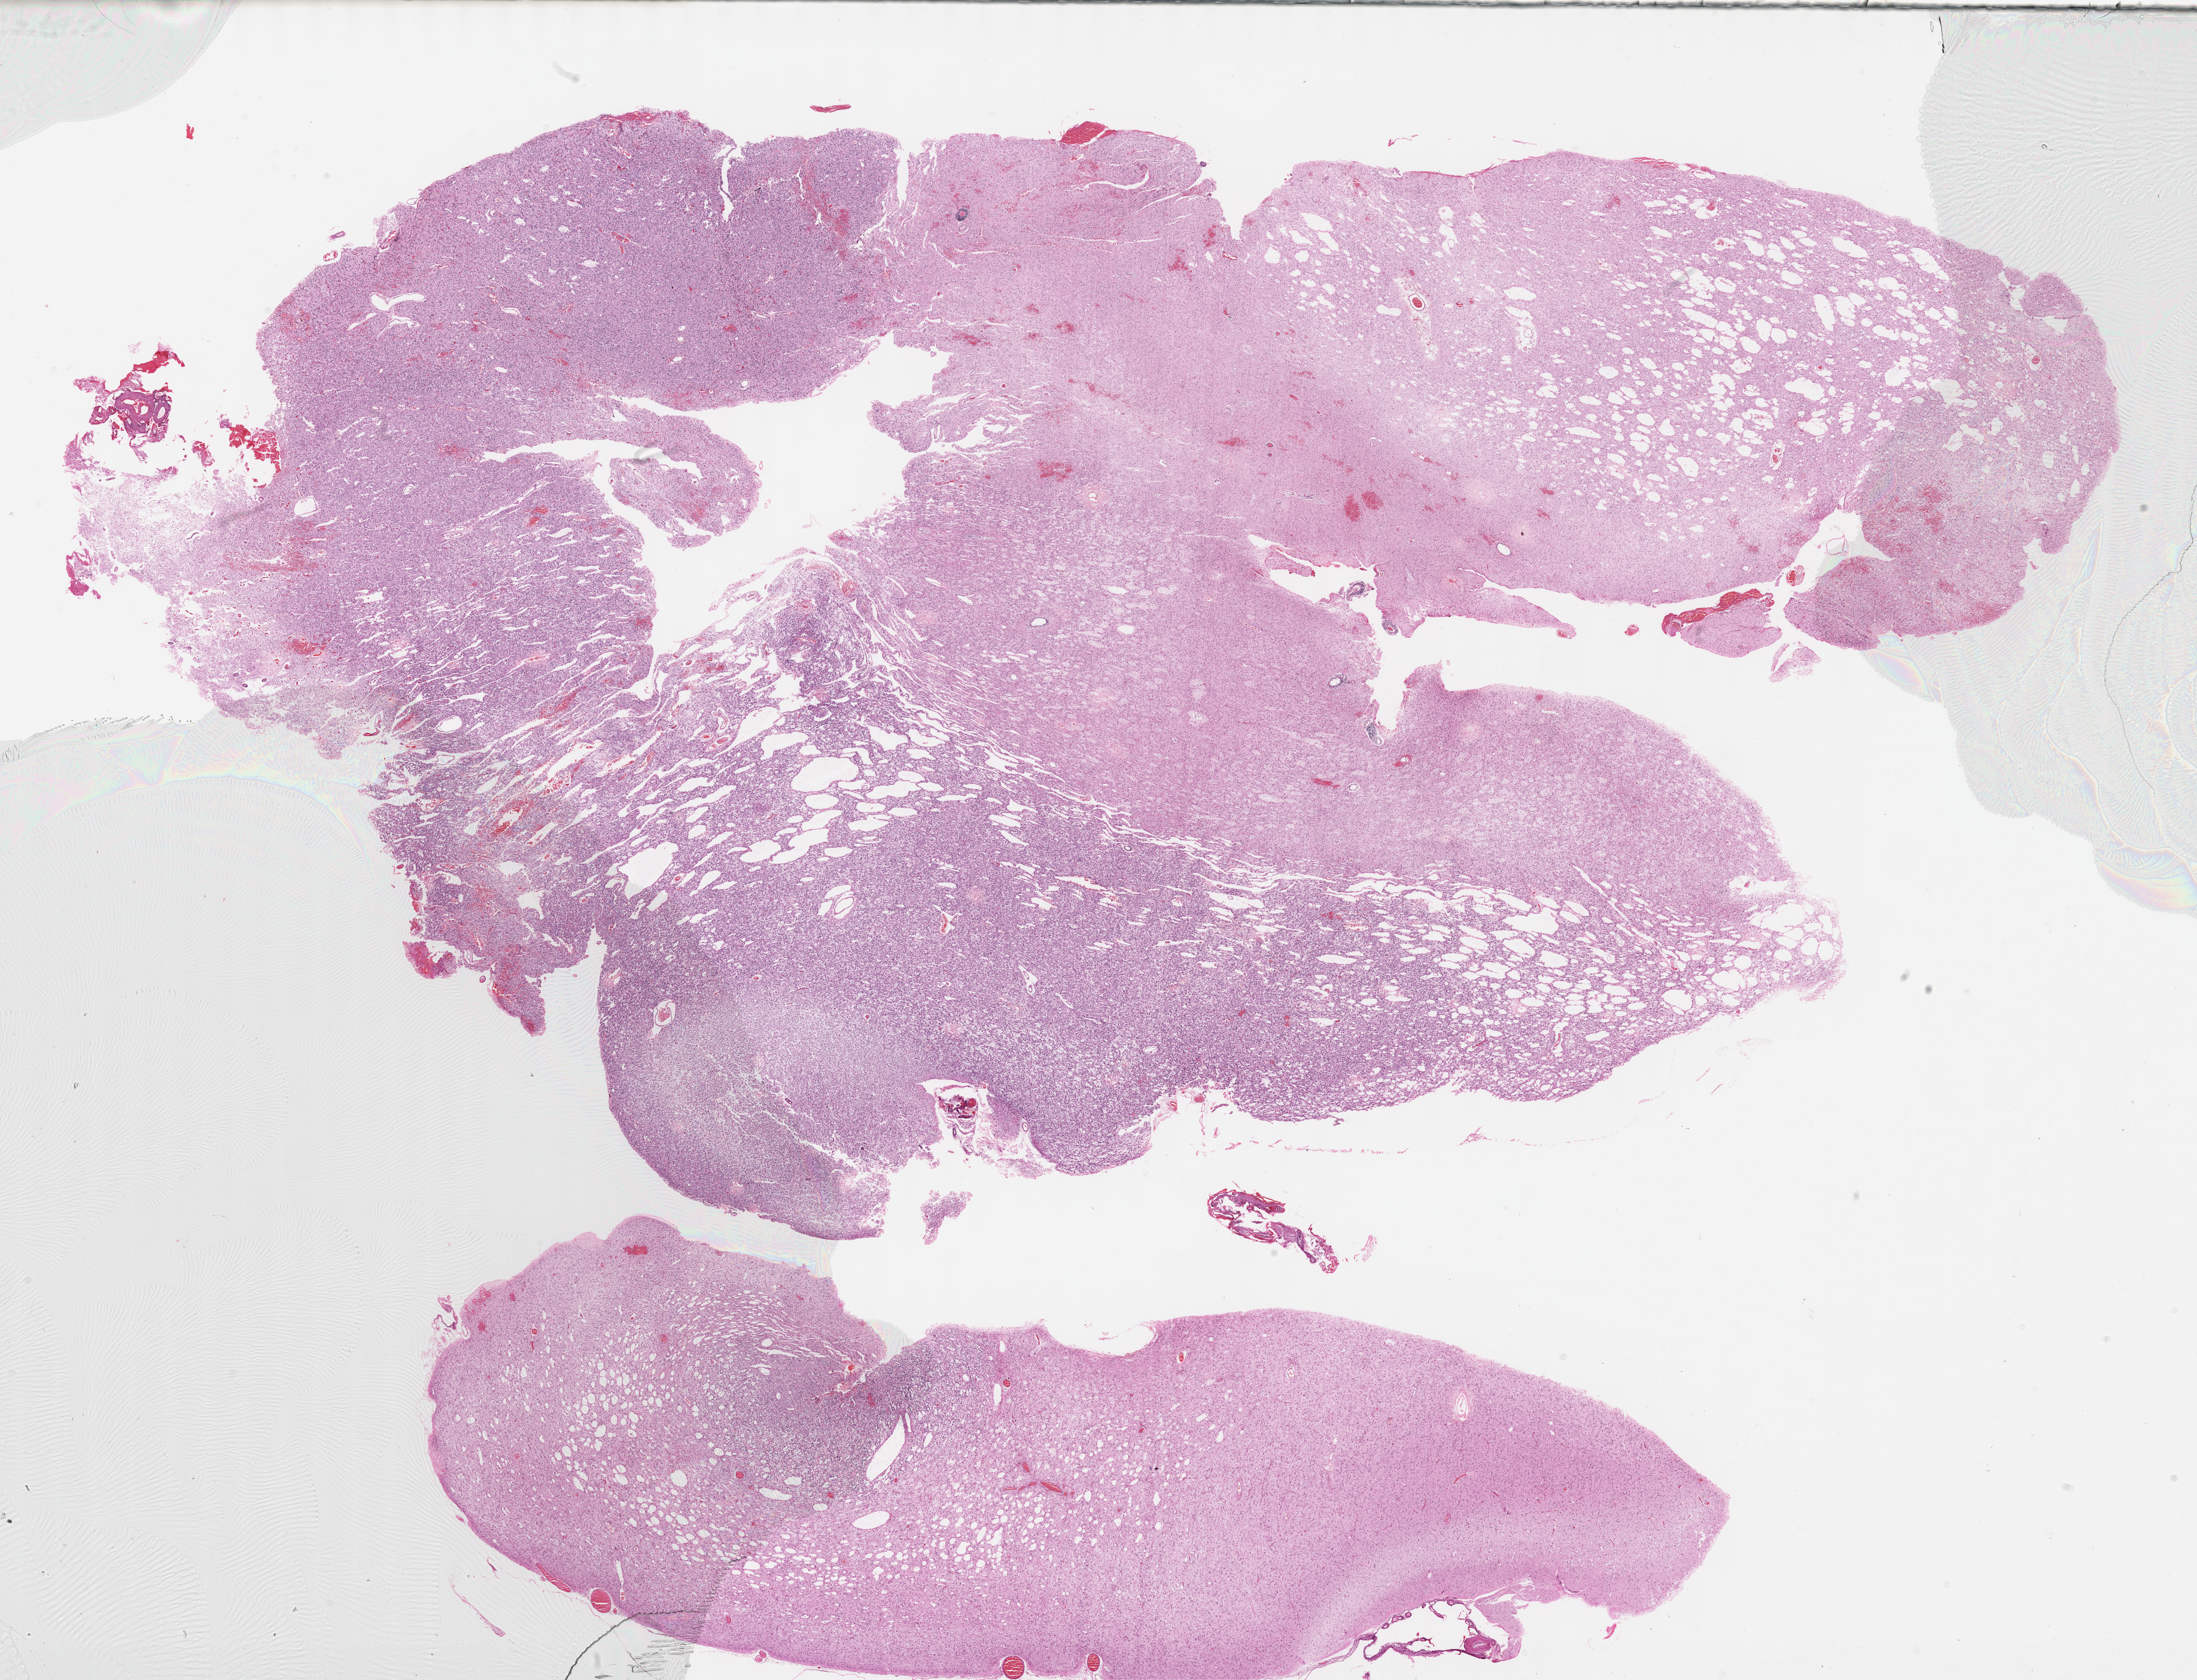
Whole-slide histology image, H&E-stained — a low-resolution overview of the entire scanned area, about 29.7 x 22.7 mm (from a 40x scan). Formalin-fixed paraffin-embedded (FFPE) diagnostic section. Primary tumour sample from the brain. Patient: female, age at initial diagnosis 25 years. Histologic grade: G2 (moderately differentiated).
• histologic diagnosis: Mixed glioma (cerebrum)